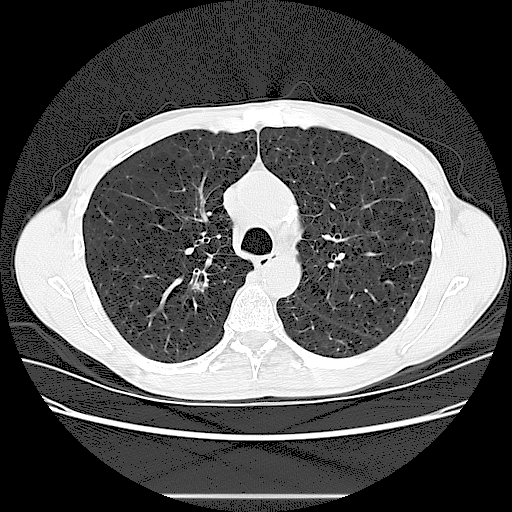
Low-dose screening chest CT, one axial slice; slice 90 of 131 in the series (ordered by position); 120 kVp; lung window (W 1500 / L -600 HU); 2.5 mm slice thickness; 512 × 512 image matrix.
Annotated regions visible in this slice (outlined manually by an expert reader):
- lesion 1 (tumor, upper lobe of right lung): bounding box <193,279,205,292> (left, top, right, bottom; pixels)